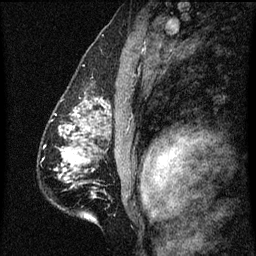
Breast MRI (dynamic contrast-enhanced), one sagittal slice; position 39 of 60 along the scan axis; dynamic contrast-enhanced series, image 2 of 3 at this slice position (ordered by acquisition); 1.5 T; TE 4.2 ms, TR 8 ms; 2 mm slice thickness; 256 × 256 image matrix, field of view 180 × 180 mm. Female patient, age 51 years.
Structures marked on this image (semi-automatically segmented with operator editing):
- analysis volume of interest (the breast-tissue region the enhancement analysis was run in; not a lesion): bounding box <61,92,102,129> (left, top, right, bottom; pixels)
- tumour enhancement mask (voxels above the 70 % enhancement threshold inside the analysis volume of interest): <70,100,102,129>